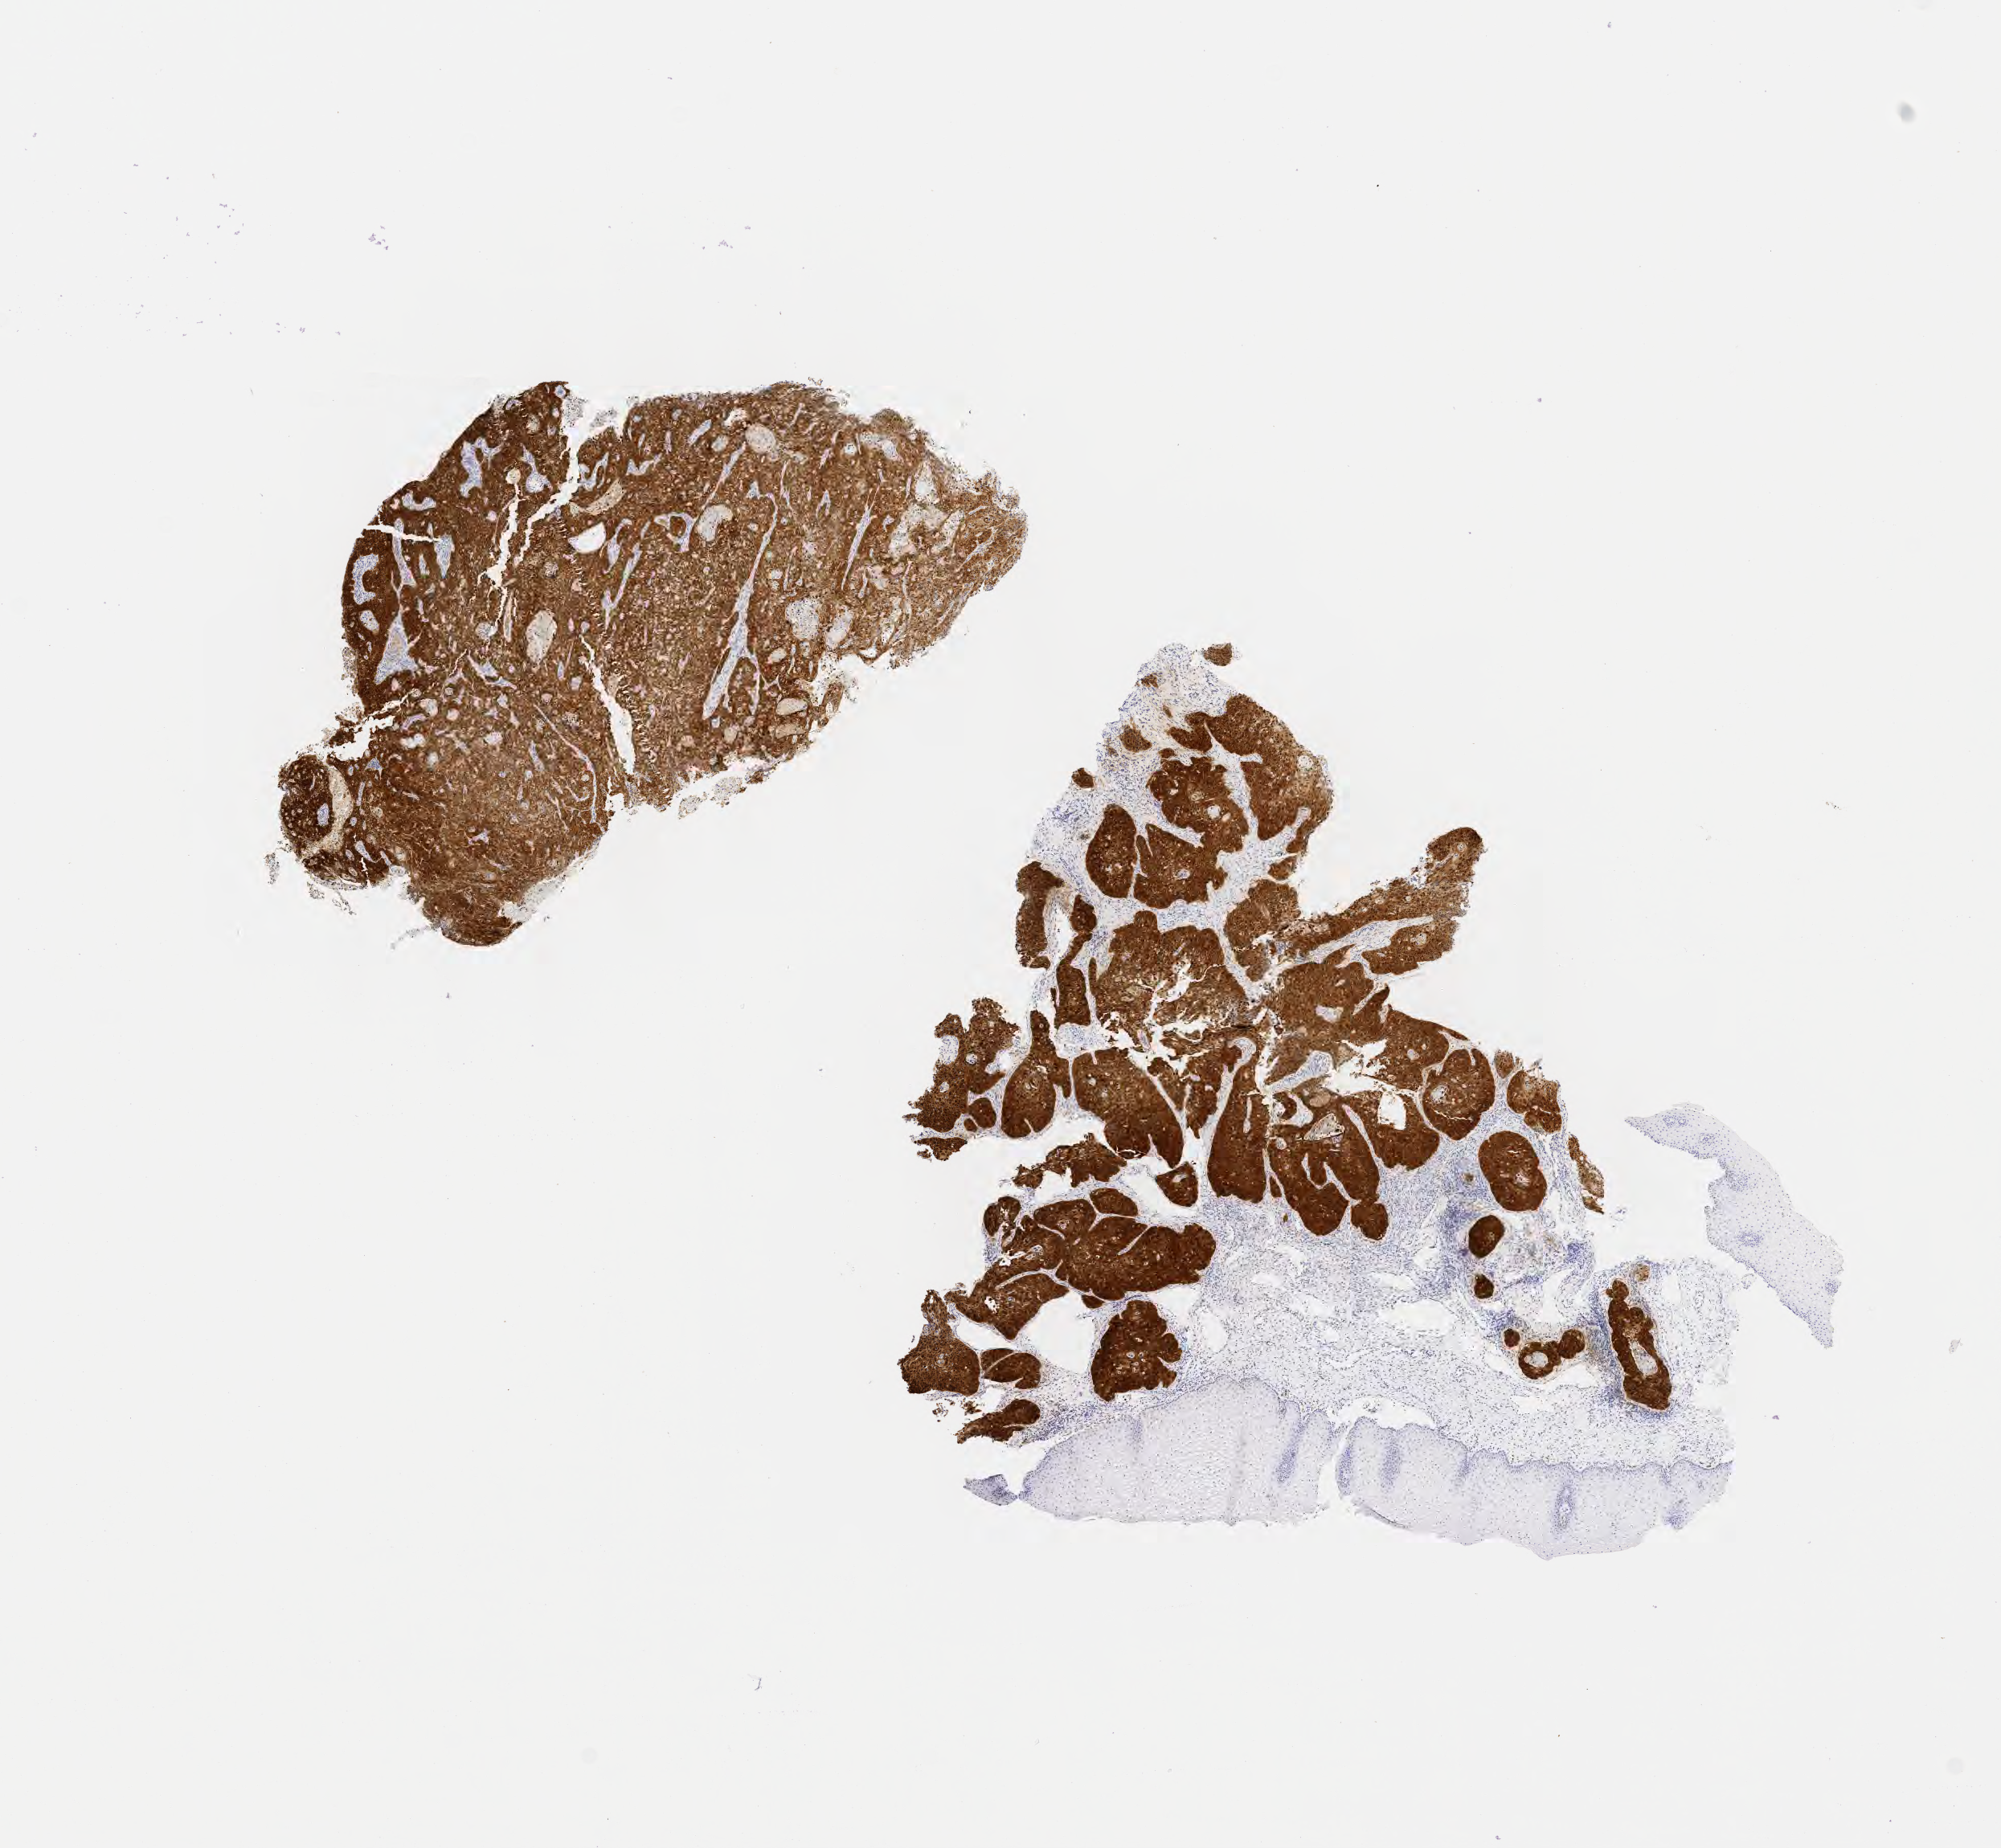
Immunohistochemistry (IHC) whole-slide image stained for p16 (p16INK4a) — whole scanned area (about 10.1 x 9.3 mm) shown as a low-resolution overview. Tumor tissue. Anatomic site: cervix. Female patient, age 35 years.
• diagnosis: Squamous cell carcinoma, keratinizing, NOS